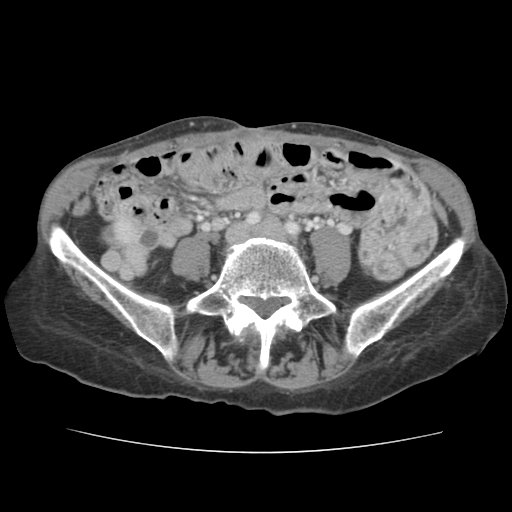
Contrast-enhanced abdominal CT, one axial slice; position 6 of 136 along the scan axis; 120 kVp; intravenous contrast given; soft-tissue window (W 400 / L 40 HU); 512 × 512 image matrix. Female patient, age 77 years. Case-level facts recorded for this patient, not image findings: diagnosis: colorectal cancer liver metastases, imaged before liver resection.
Structures marked on this image (outlined manually by an expert reader):
- liver: box from (x=118, y=218) to (x=133, y=239) px